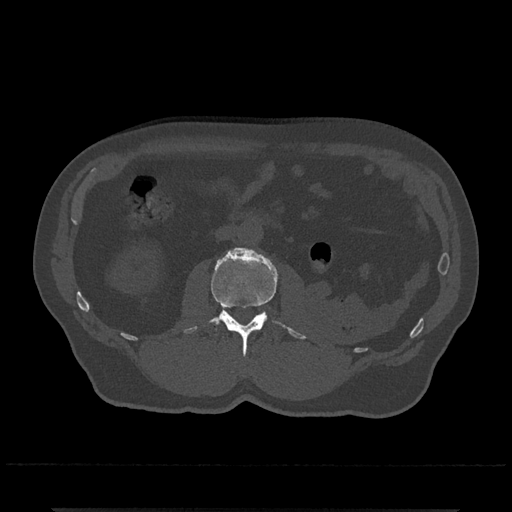
CT including the spine, one axial slice; position 286 of 797 along the scan axis; reconstruction kernel Br40s/3; 120 kVp; bone window (W 1800 / L 400 HU); 0.5 mm slice thickness; 512 × 512 image matrix. Male patient, age 67 years. From the clinical record (not read from this slice): primary cancer: prostate.
Annotated regions visible in this slice (semi-automatic segmentation, software-assisted and operator-edited):
- L2 vertebra: bounding box (x1, y1, x2, y2) in pixels: (184, 247, 306, 356)